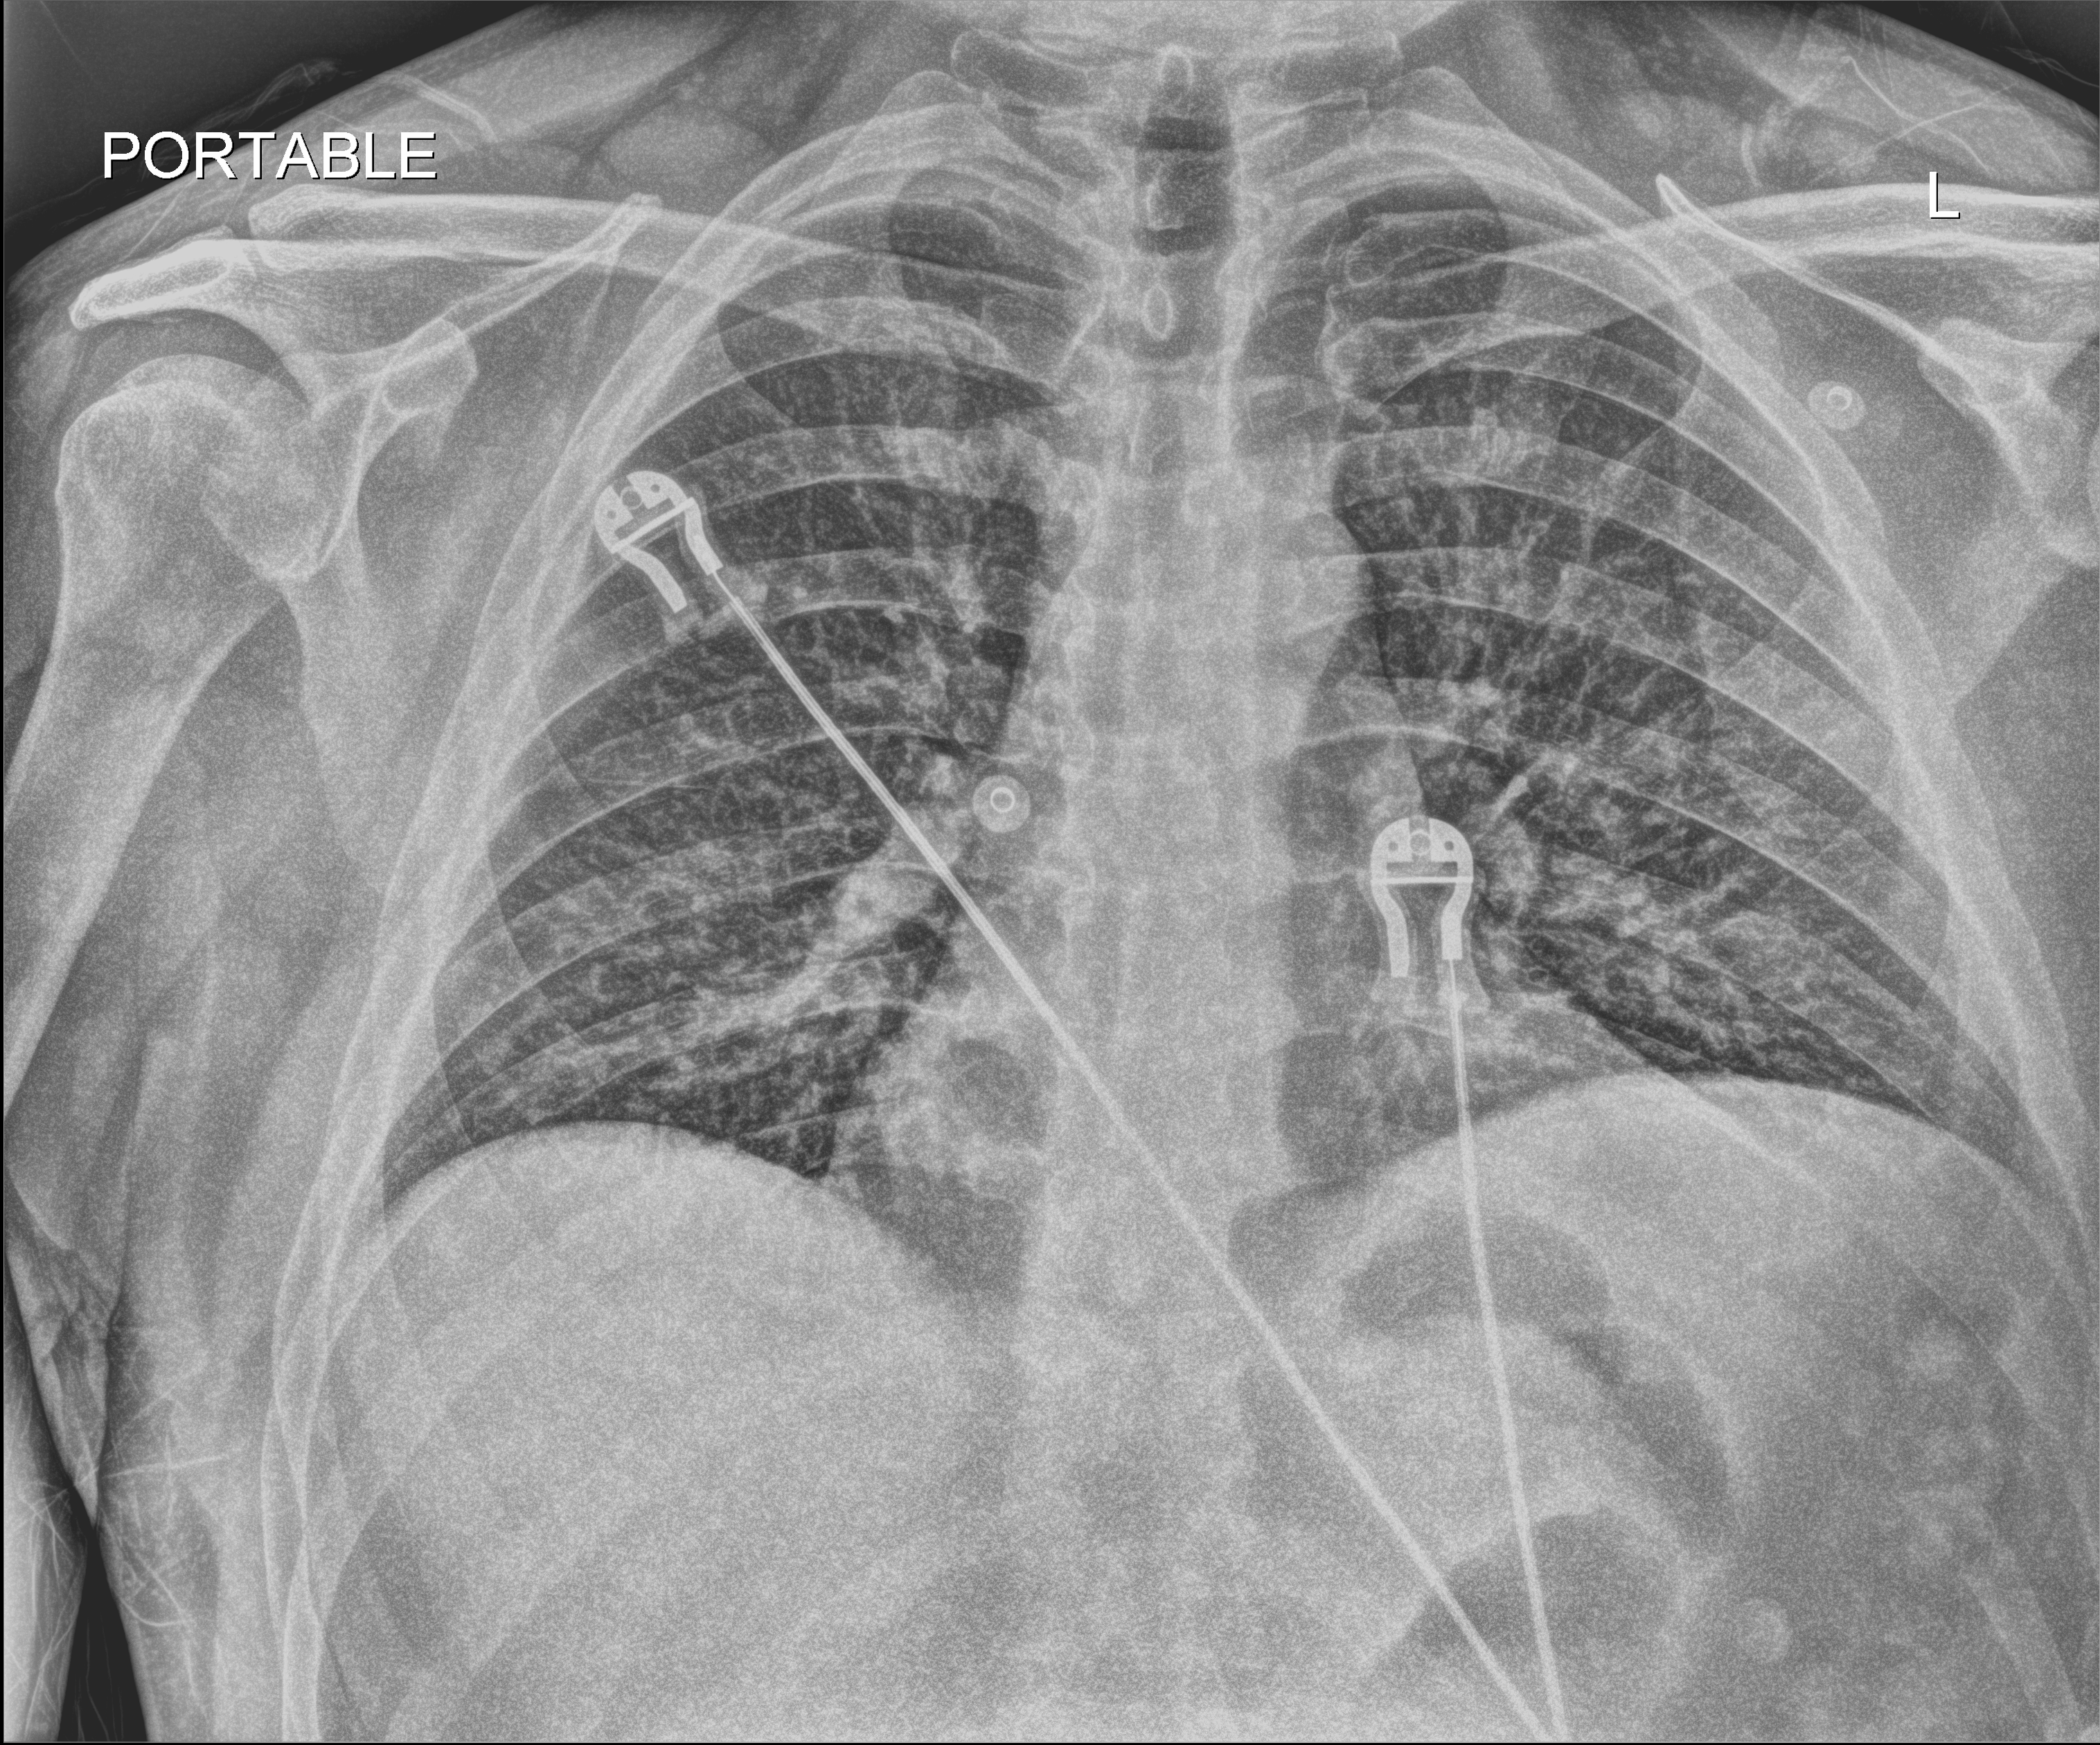
Chest X-ray; anteroposterior (AP) projection. Male patient hospitalised with COVID-19, age 18–59 years.
From the hospital-stay record, not from the radiograph (when in the stay this image was taken is not recorded): admitted to intensive care during this hospital stay: no; mechanically ventilated during this hospital stay: no.